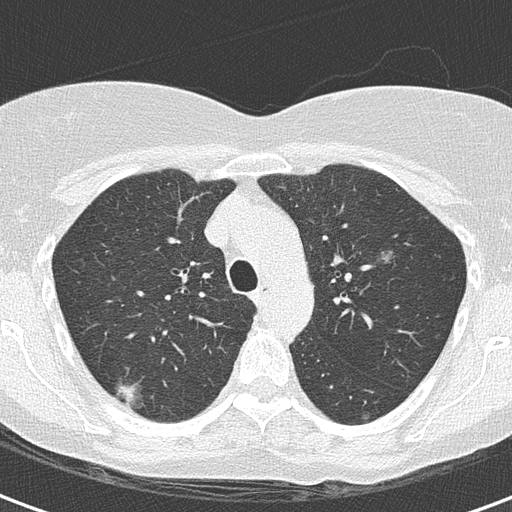
Axial slice from a low-dose chest CT screening exam, second screening round (one year after baseline), lung window (W 1500 / L -600 HU), 120 kVp. Female, age 56 years at enrolment. Current smoker at enrolment.
• Expert reader's lesion annotation, bounding box <91,366,152,417> (left, top, right, bottom; pixels).
• Reader record for this screening exam (exam-level; its link to the box is not recorded): non-calcified nodule or mass ≥4 mm, right upper lobe, 18 × 18 mm, mixed attenuation, pre-existing on the prior screen: yes.
• Official screen result: positive, other.
• Participant outcome: lung cancer diagnosed 93 days after this screen — bronchiolo-alveolar adenocarcinoma, NOS, right upper lobe, well differentiated (G1), stage IA (AJCC 6th edition), 15 mm at pathology.